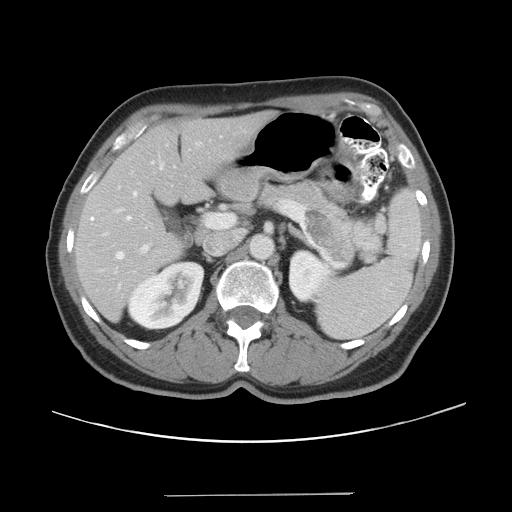
Contrast-enhanced abdominal CT, one axial slice; position 22 of 43 along the scan axis; reconstruction kernel STANDARD; intravenous contrast given; soft-tissue window (W 400 / L 40 HU); 5 mm slice thickness; 512 × 512 image matrix, field of view 409 × 409 mm. Male patient, age 65 years. Case-level facts recorded for this patient, not image findings: diagnosis: colorectal cancer liver metastases, imaged before liver resection; multiple liver metastases: no; largest metastasis: 3.8 cm; disease in both lobes: no.
Outlined on this slice (expert manual segmentation):
- hepatic veins: bounding box <113,190,138,259> (left, top, right, bottom; pixels)
- liver: <75,112,270,318>
- planned liver remnant (the part of the liver to remain after resection): <75,112,270,318>
- portal vein (with intrahepatic branches): <103,161,154,253>